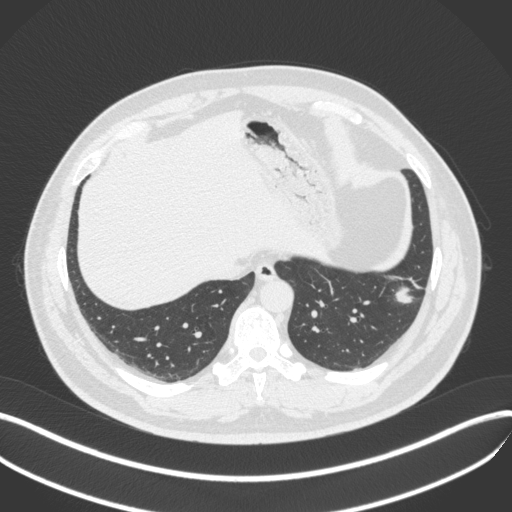
Chest CT, one axial slice. Position 109 of 420 along the scan axis. Reconstruction kernel B31f. 120 kVp. Lung window (W 1500 / L -600 HU). 1 mm slice thickness. 512 × 512 image matrix, field of view 400 × 400 mm. Male patient, age 39 years. Case-level facts recorded for this patient, not image findings: clinical TNM (as recorded): T2a N0 M0; histopathological grade: G2-3.
Outlined on this slice (bounding box drawn by a radiologist):
- lung tumour (recorded histology: adenocarcinoma): bounding box <392,281,417,312> (left, top, right, bottom; pixels)